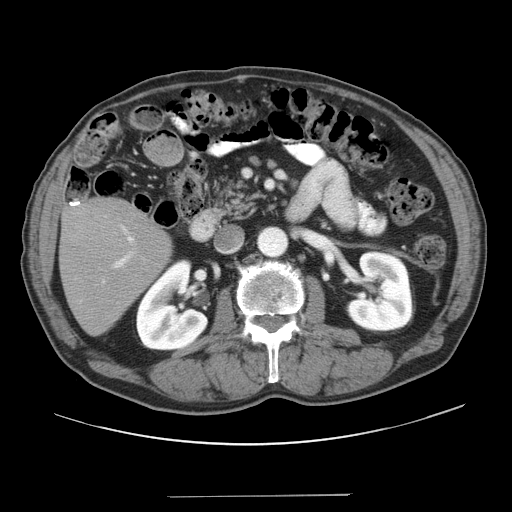
Contrast-enhanced abdominal CT, one axial slice. Position 13 of 41 along the scan axis. Reconstruction kernel STANDARD. 120 kVp. Intravenous contrast given. Soft-tissue window (W 400 / L 40 HU). 5 mm slice thickness. 512 × 512 image matrix, field of view 420 × 420 mm. Male patient, age 75 years. From the clinical record (not read from this slice): diagnosis: colorectal cancer liver metastases, imaged before liver resection; multiple liver metastases: no.
Structures marked on this image (manually delineated by an expert):
- liver: bounding box (x1, y1, x2, y2) in pixels: (60, 199, 172, 335)
- planned liver remnant (the part of the liver to remain after resection): (60, 199, 172, 335)
- portal vein (with intrahepatic branches): (102, 225, 134, 284)